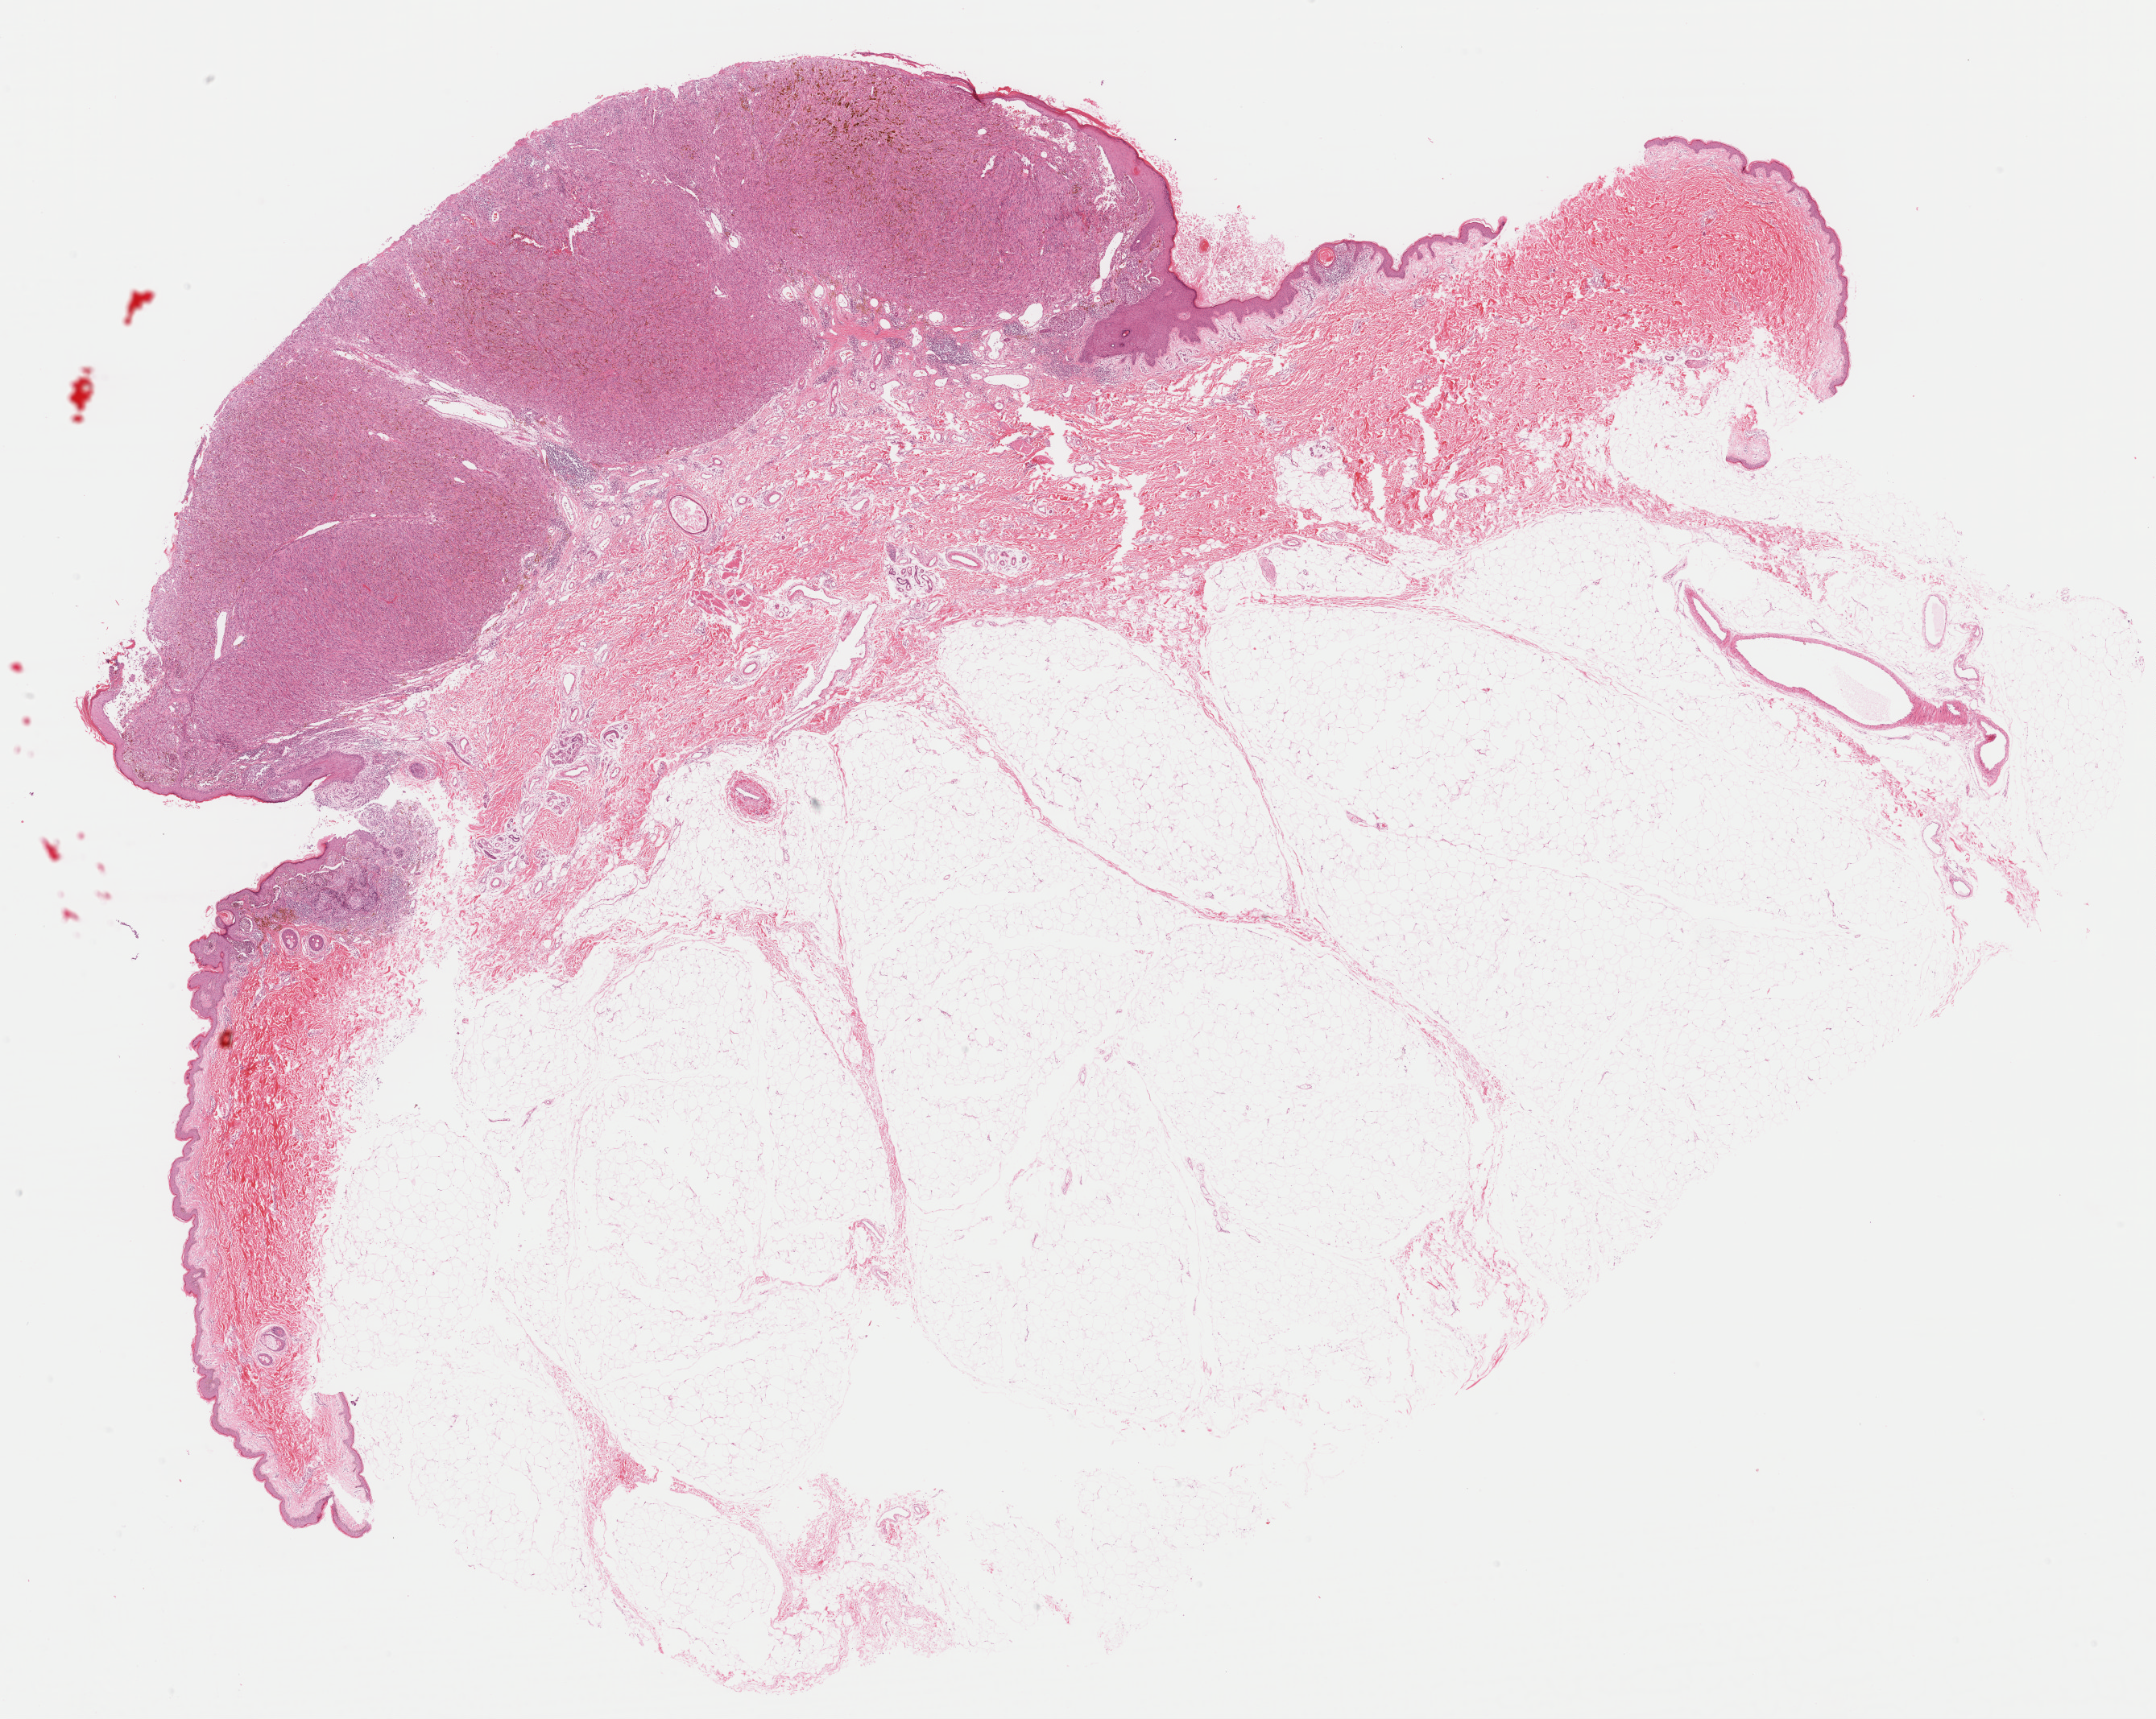
Digitized H&E tissue section (whole slide) — a low-resolution overview of the entire scanned area, about 21.1 x 16.9 mm (acquisition: 40x scan); formalin-fixed paraffin-embedded (FFPE) diagnostic section; skin, primary tumour sample. Patient: female, age at initial diagnosis 77 years.
Histologic diagnosis: Malignant melanoma, NOS.